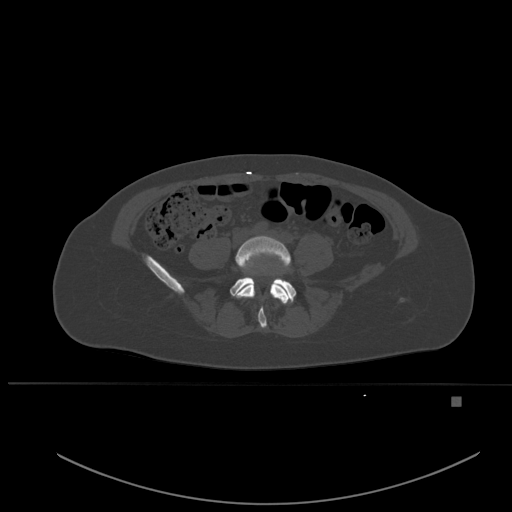
CT including the spine, one axial slice; slice 164 of 651 in the series (ordered by position); bone window (W 1800 / L 400 HU); 1.5 mm slice thickness; 512 × 512 image matrix, field of view 443 × 443 mm. Patient: female, 49 years. Case-level facts recorded for this patient, not image findings: primary cancer: breast; vertebrae with lytic lesions (as recorded): L3, T12, L4.
Structures marked on this image (semi-automatic segmentation, software-assisted and operator-edited):
- L4 vertebra: bounding box [x1, y1, x2, y2] px = [236, 236, 291, 328]
- L5 vertebra: [230, 262, 296, 302]